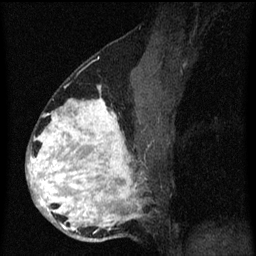
Breast MRI (dynamic contrast-enhanced), one sagittal slice; slice 36 of 60 in the series (ordered by position); dynamic contrast-enhanced series, image 2 of 3 at this slice position (ordered by acquisition); 1.5 T; TE 4.2 ms, TR 8.4 ms; 256 × 256 image matrix, field of view 180 × 180 mm. Patient: female, 34 years. From the clinical record (not read from this slice): setting: breast cancer imaged before/during neoadjuvant chemotherapy; receptor status: HR-positive, HER2-negative.
Annotated regions visible in this slice (semi-automatic segmentation, software-assisted and operator-edited):
- analysis volume of interest (the breast-tissue region the enhancement analysis was run in; not a lesion): bounding box <28,58,157,243> (left, top, right, bottom; pixels)
- tumour enhancement mask (voxels above the 70 % enhancement threshold inside the analysis volume of interest): <28,86,141,231>